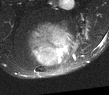
MRI of an extremity soft-tissue mass, one axial slice. Position 36 of 52 along the scan axis. T2-weighted fat-saturated. MR volume resampled by the dataset authors to the PET/CT grid (not the native acquisition matrix). 3.27 mm slice thickness. 109 × 95 image matrix, field of view 106 × 93 mm. Male patient. Case-level facts recorded for this patient, not image findings: histological type: synovial sarcoma; site of the primary tumour: left poplietal fossa.
Outlined on this slice (expert contour drawn on MRI and transferred to this co-registered scan by the dataset authors):
- gross tumour volume (mass): box from (x=28, y=24) to (x=68, y=66) px